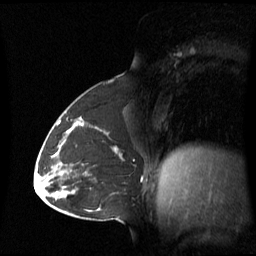
Breast MRI (dynamic contrast-enhanced), one sagittal slice. Slice 32 of 60 in the series (ordered by position). Dynamic contrast-enhanced series, image 2 of 3 at this slice position (ordered by acquisition). 1.5 T. TE 4.2 ms, TR 8.4 ms. 2.8 mm slice thickness. 256 × 256 image matrix, field of view 270 × 270 mm. Female patient, age 43 years. From the clinical record (not read from this slice): setting: breast cancer imaged before/during neoadjuvant chemotherapy; receptor status: triple-negative.
Annotated regions visible in this slice (semi-automatically segmented with operator editing):
- analysis volume of interest (the breast-tissue region the enhancement analysis was run in; not a lesion): bounding box <62,124,123,180> (left, top, right, bottom; pixels)
- tumour enhancement mask (voxels above the 70 % enhancement threshold inside the analysis volume of interest): <80,124,118,152>